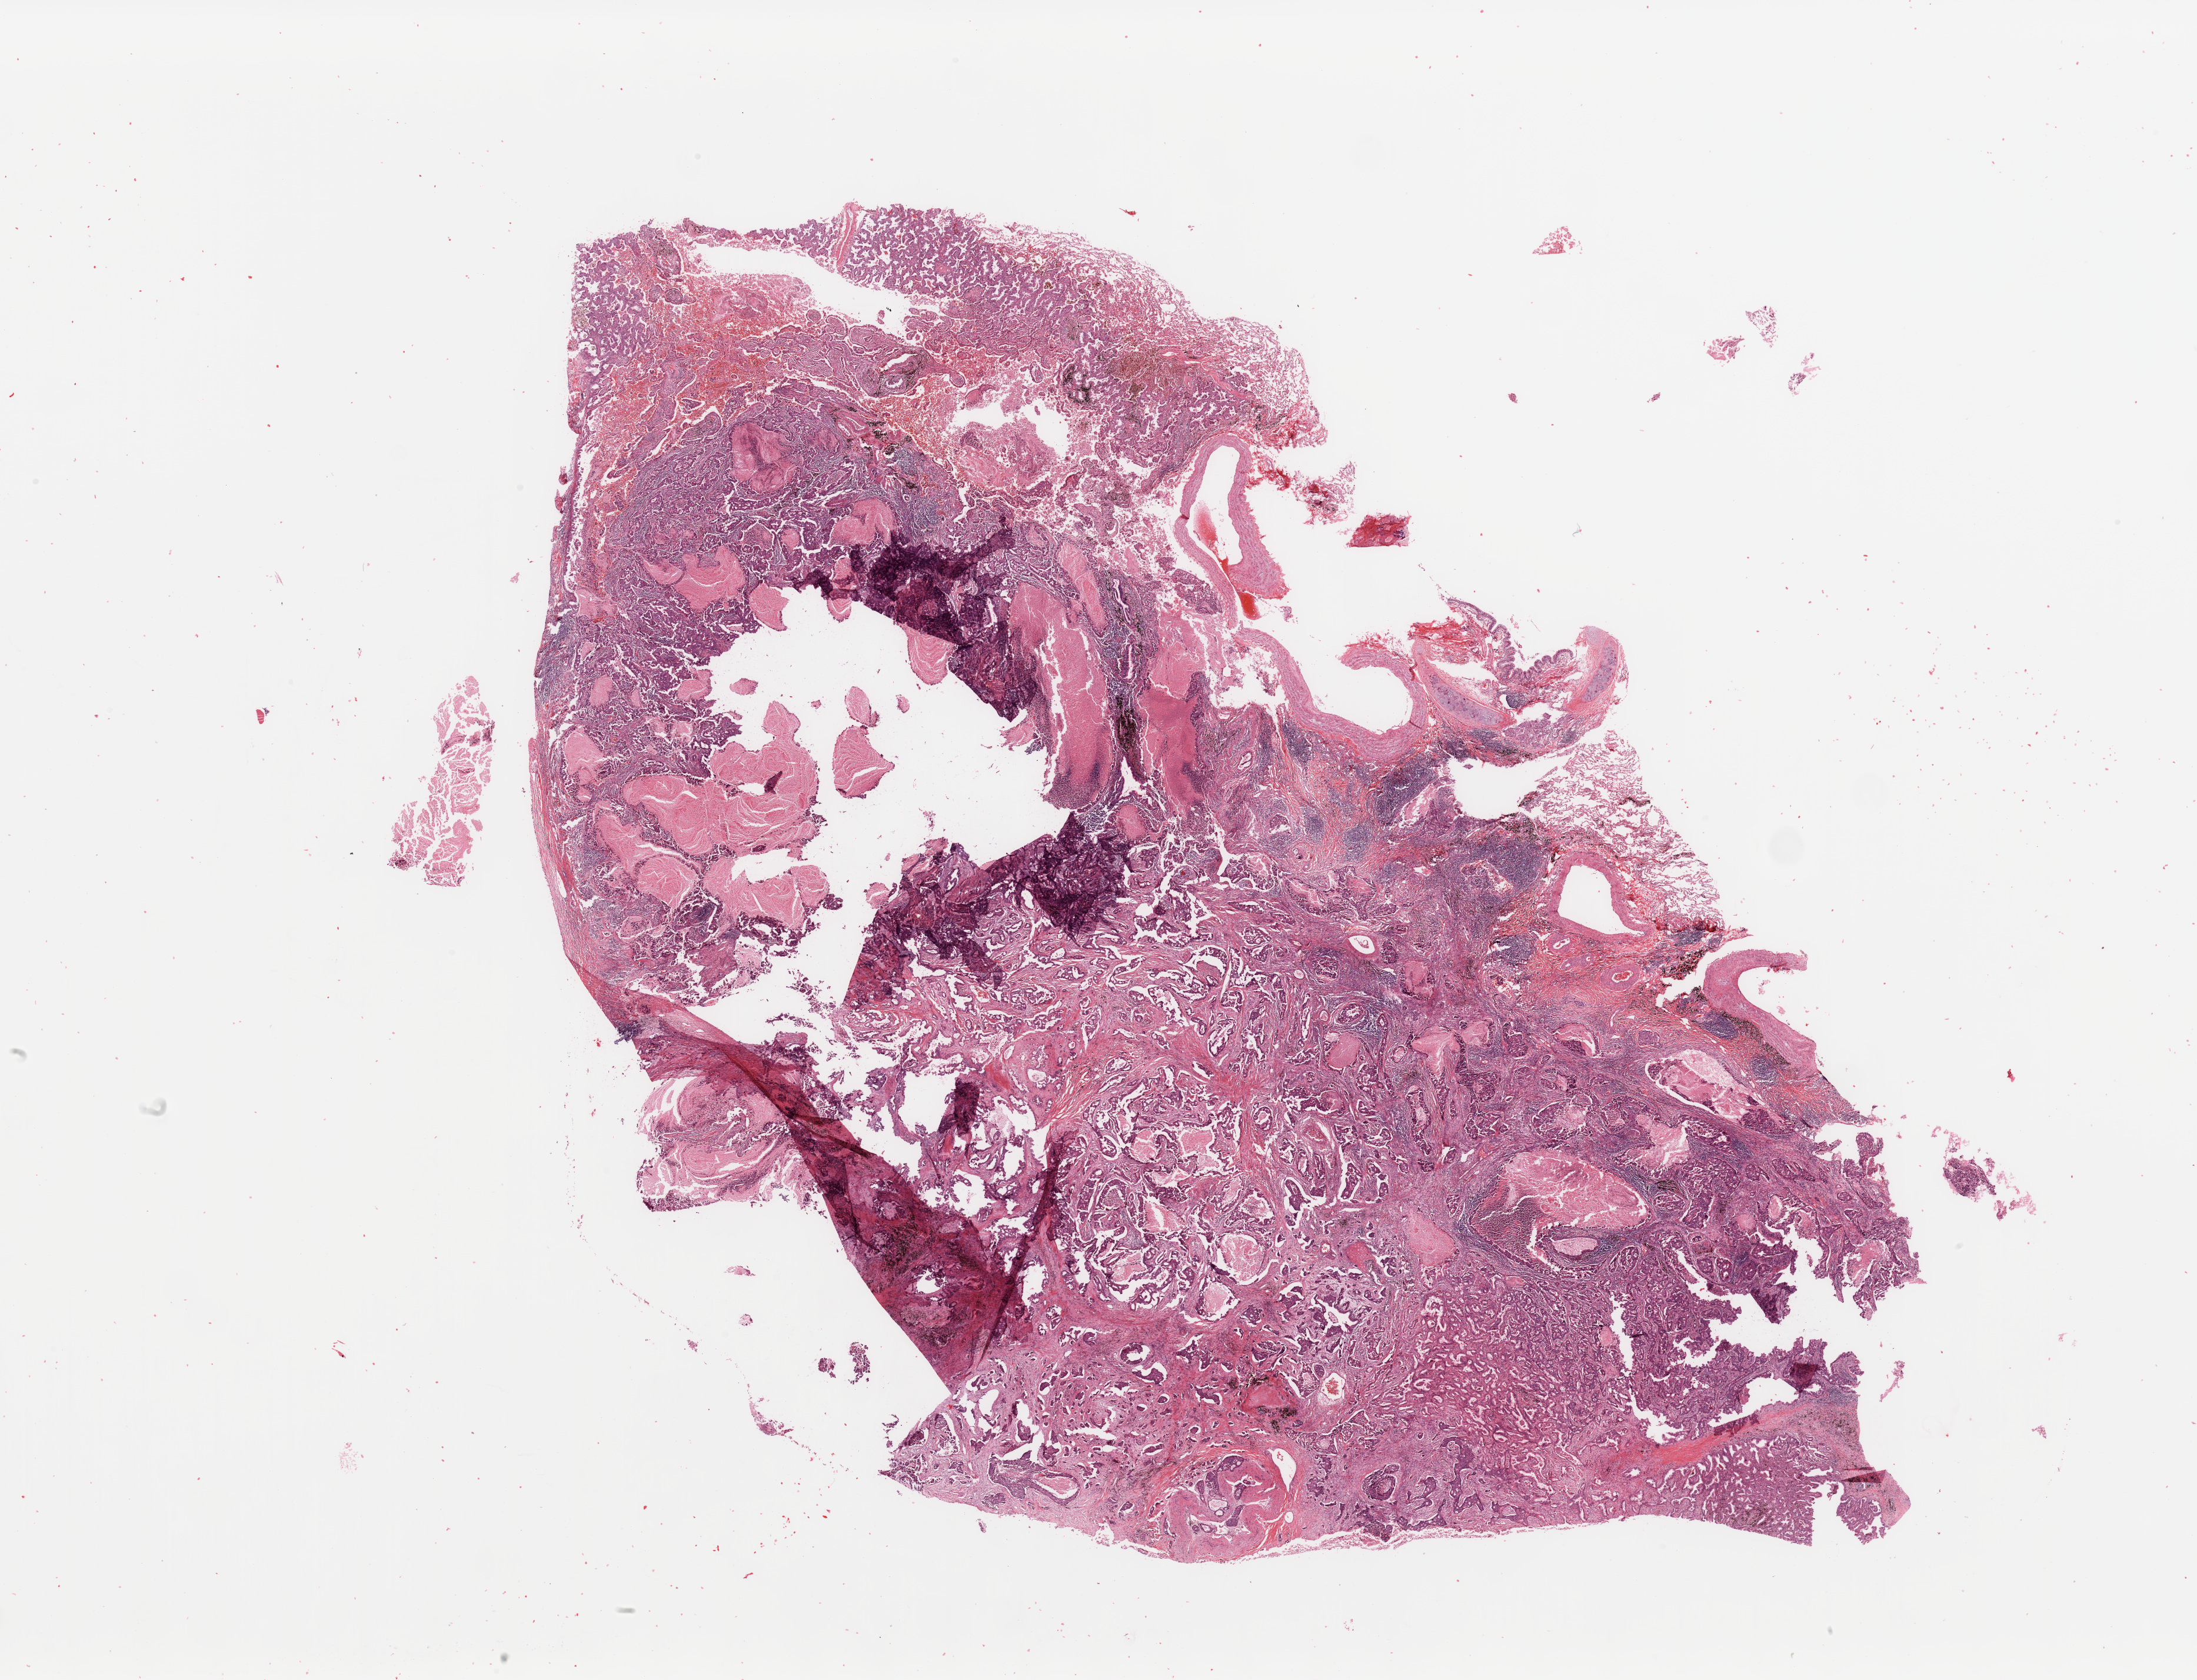
H&E-stained whole-slide image, shown as a low-resolution overview of the whole scanned area (about 29.5 x 22.6 mm, slide scanned at 20x); lung, tumour tissue. Patient: female, age 68 years. Histologic grade: G2 (moderately differentiated).
AJCC pathologic stage: IB. Diagnosis: Adenocarcinoma, NOS.